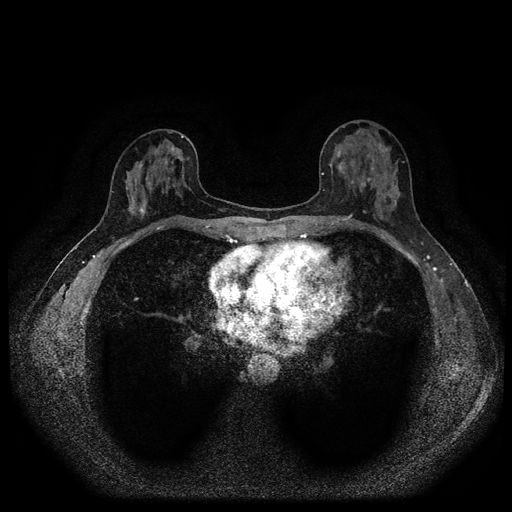
Breast MRI (dynamic contrast-enhanced, multi-phase), one axial slice; position 41 of 116 along the scan axis; dynamic contrast-enhanced series, time point 2 of 5 at this slice position (early post-contrast); 1.5 T; TE 2.7 ms, TR 5.4 ms; 2 mm slice thickness; 512 × 512 image matrix, field of view 330 × 330 mm. Patient: female, 42 years.
Structures marked on this image (semi-automatically segmented with operator editing):
- breast lesion (labelled benign in the annotation): box from (x=378, y=143) to (x=391, y=154) px